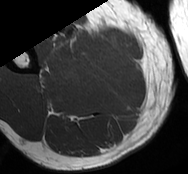
MRI of an extremity soft-tissue mass, one axial slice. Position 20 of 93 along the scan axis. MR volume resampled by the dataset authors to the PET/CT grid (not the native acquisition matrix). 3.27 mm slice thickness. 188 × 174 image matrix, field of view 184 × 170 mm. Male patient. Case-level facts recorded for this patient, not image findings: histological type: undifferentiated - pleiomorphic; grade: high; site of the primary tumour: right thigh.
Annotated regions visible in this slice (expert contour drawn on MRI and transferred to this co-registered scan by the dataset authors):
- gross tumour volume including surrounding oedema: bounding box [x1, y1, x2, y2] px = [52, 42, 117, 68]